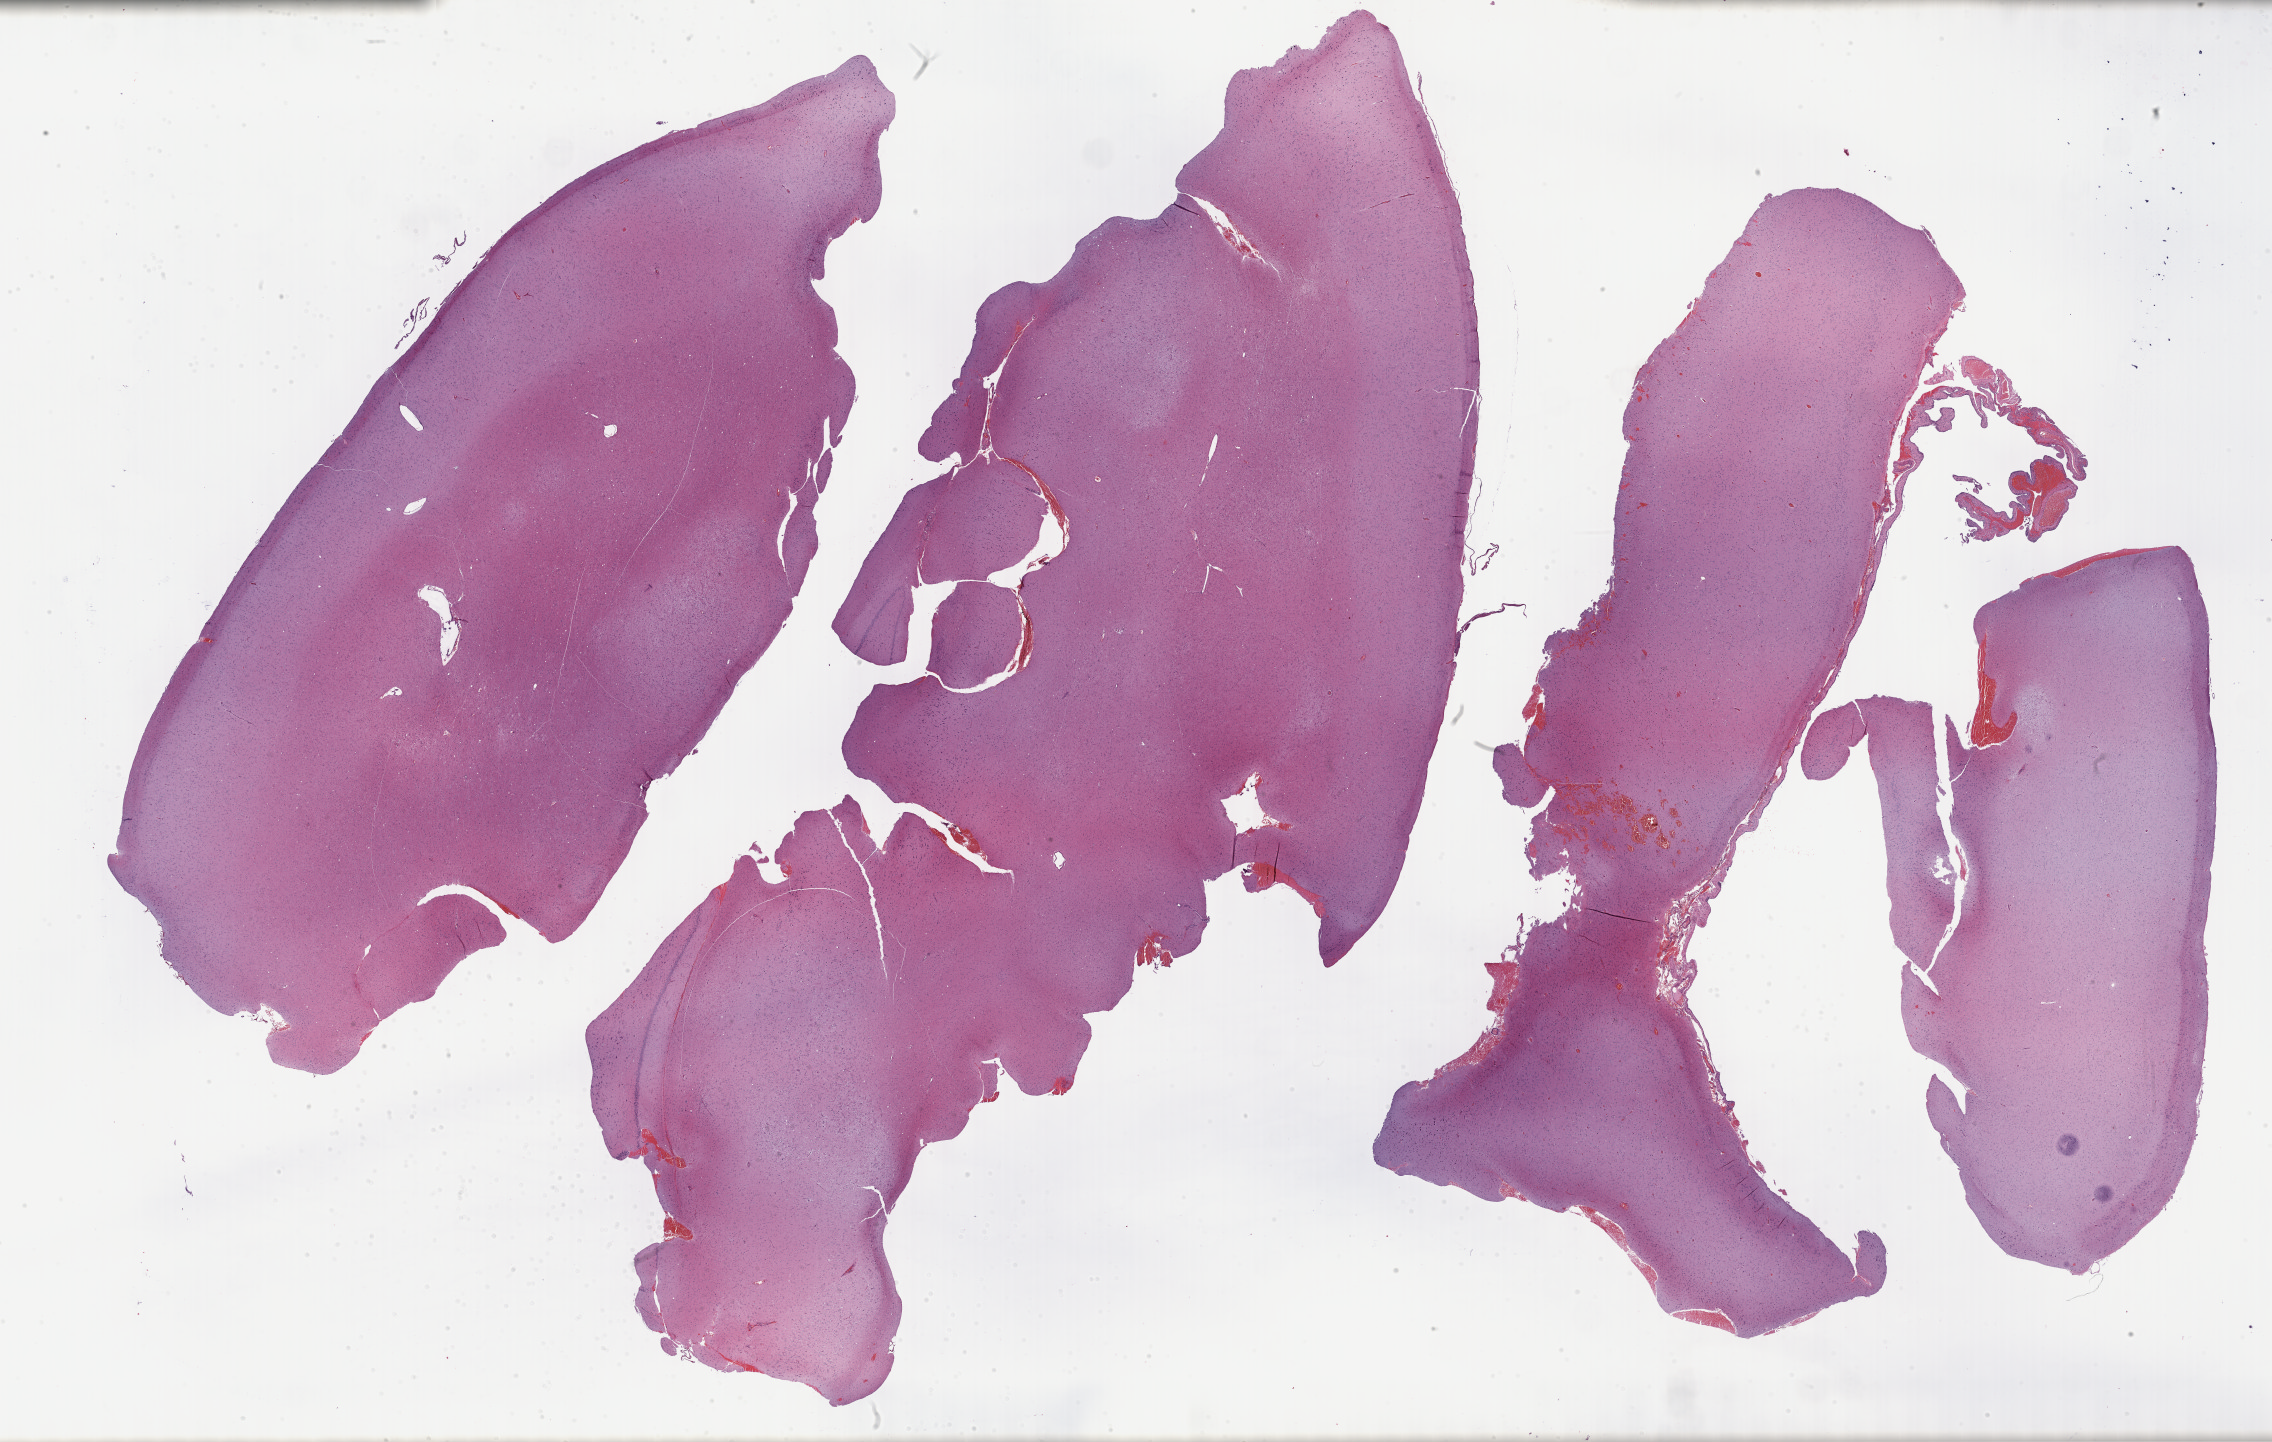
Hematoxylin and eosin (H&E) stained whole-slide image — a low-resolution overview of the entire scanned area, about 36.7 x 23.3 mm. FFPE section. Primary tumour sample from the brain. Female, age 37 years at initial diagnosis. Histologic grade: G2 (moderately differentiated).
Diagnosis: Astrocytoma, NOS (cerebrum).